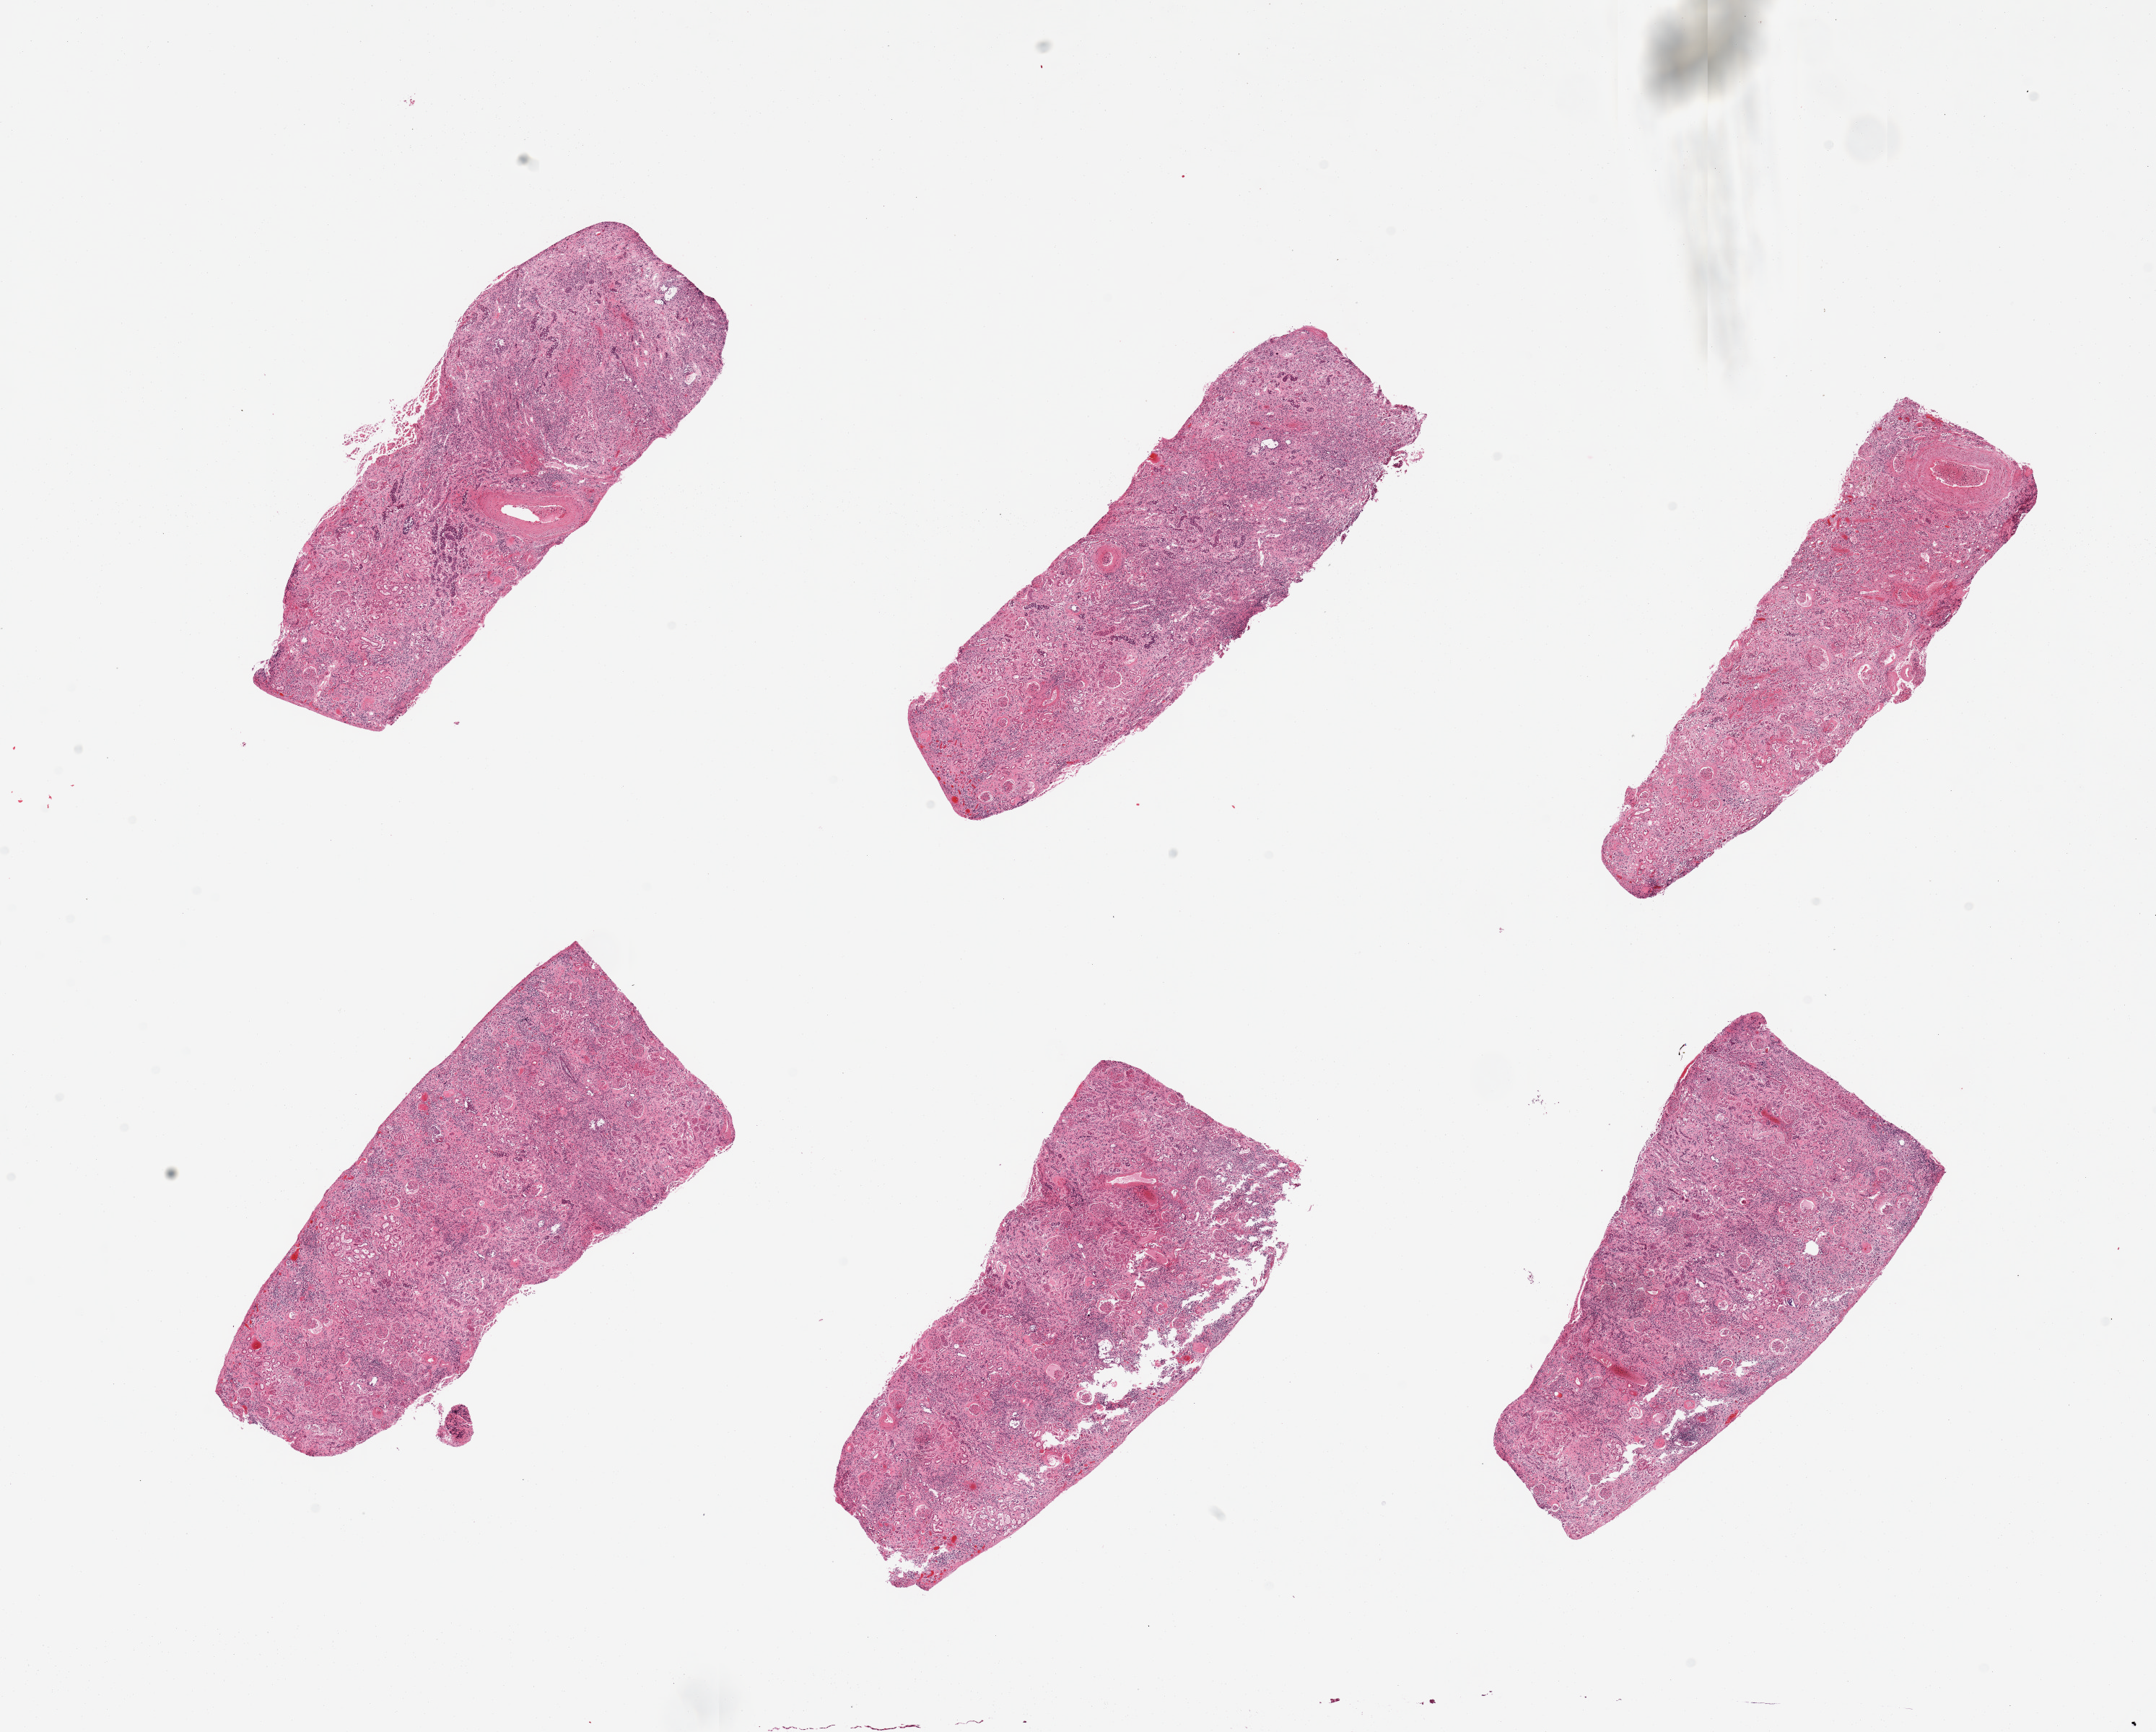
Digitized haematoxylin and eosin-stained section, brightfield — low-resolution overview of the scanned area, about 23.6 x 19.0 mm (from a 20x scan); PAXgene-fixed, paraffin-embedded tissue; section of renal cortex (target tissue); donor tissue sample. Female donor.
Review note (as recorded): 6 pieces; chronic inflammation.